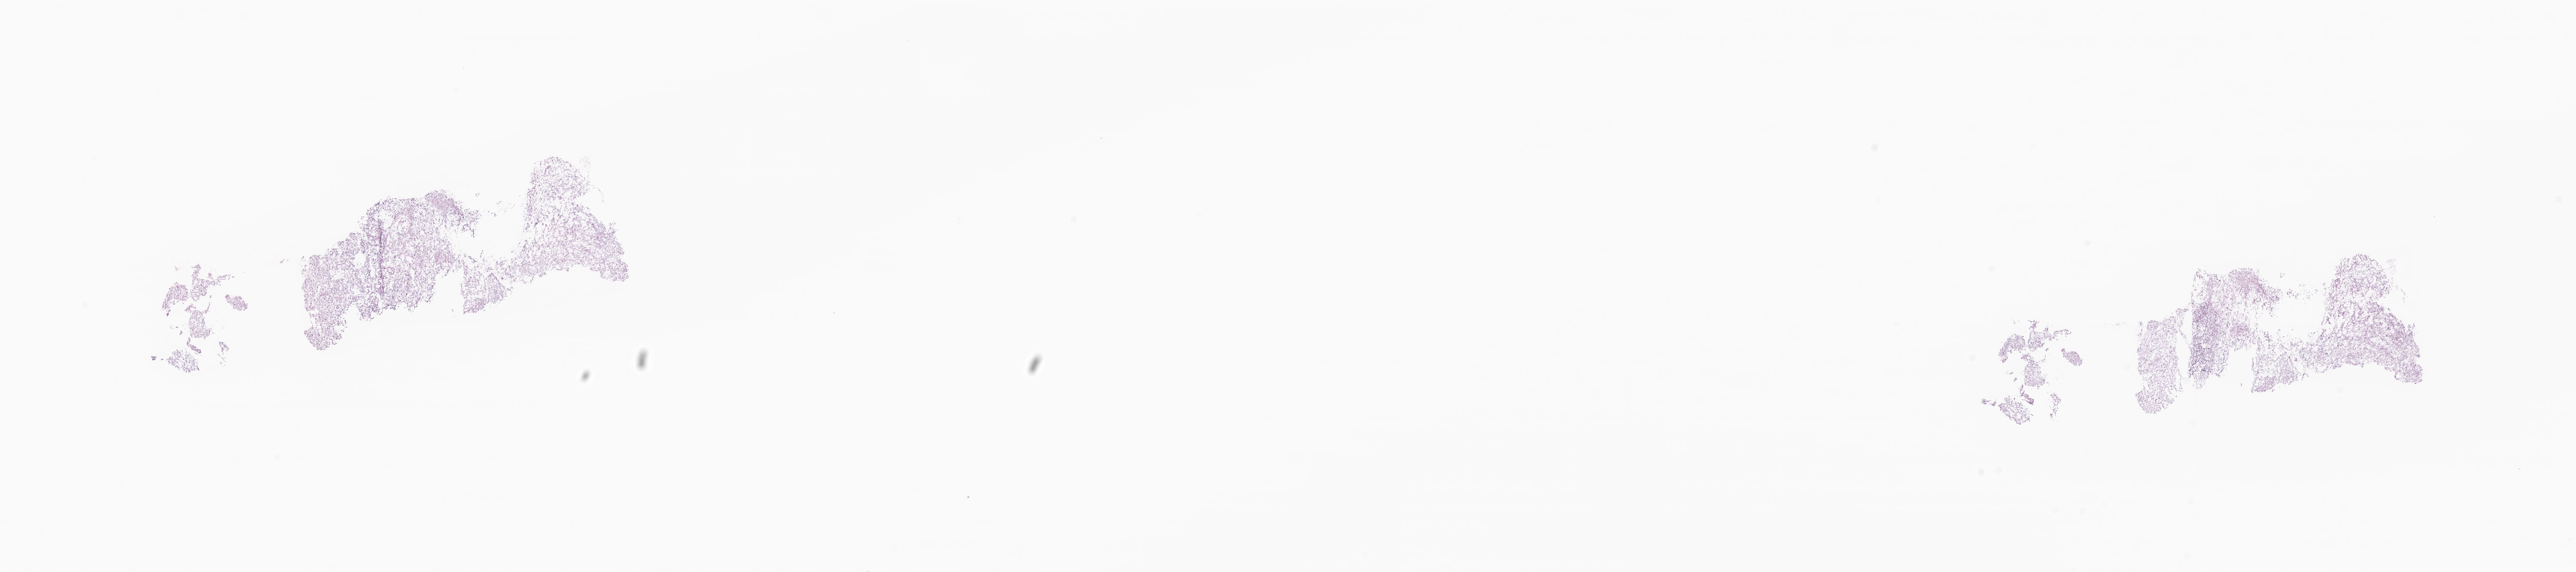
Hematoxylin and eosin (H&E) whole-slide image of tumor tissue from the brain — a low-resolution overview of the entire scanned area, about 32.9 x 7.3 mm, frozen section. Male patient, age 139 months (11 years 7 months).
Diagnosis (ICD-O-3 morphology term): Pilocytic astrocytoma.